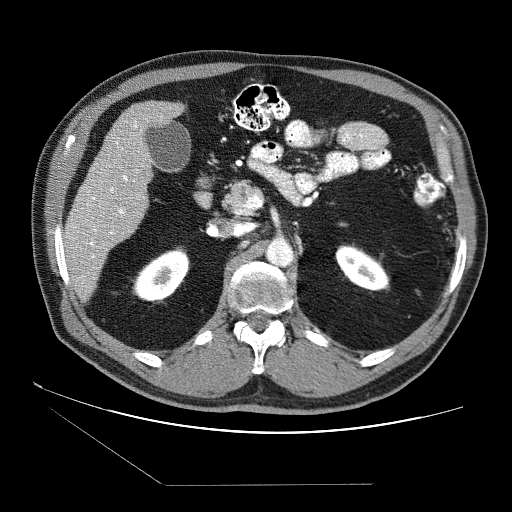
Contrast-enhanced abdominal CT (liver protocol), one axial slice; position 29 of 87 along the scan axis; 120 kVp; soft-tissue window (W 400 / L 40 HU); 512 × 512 image matrix, field of view 400 × 400 mm. From the clinical record (not read from this slice): diagnosis: hepatocellular carcinoma (patient treated with transarterial chemoembolisation; whether this scan precedes or follows treatment is not stated here); TNM stage (as recorded): Stage-II; Child-Pugh class: B; tumour differentiation: no biopsy; tumour nodularity: multinodular.
Outlined on this slice (semi-automatic segmentation, software-assisted and operator-edited):
- liver parenchyma outside the tumour (the mass and vessels are separate outlines, so this box may not span the whole liver): bounding box [x1, y1, x2, y2] px = [64, 100, 184, 296]
- liver vessels: [67, 116, 162, 258]